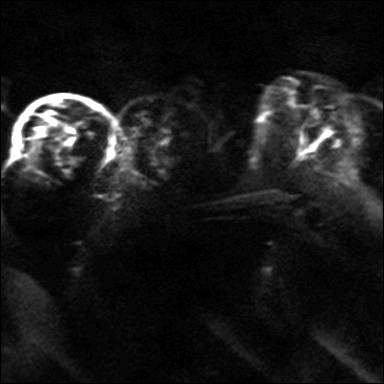
Breast MRI, one axial slice. Slice 23 of 36 in the series (ordered by position). Diffusion-weighted series; image 2 of 4 stored at this slice position (different b-values; order by instance number). 3 T. 4 mm slice thickness. 384 × 384 image matrix, field of view 320 × 320 mm. Female patient.
Structures marked on this image (manually delineated by an expert):
- tumour on diffusion-weighted imaging: bounding box [x1, y1, x2, y2] px = [64, 156, 80, 164]